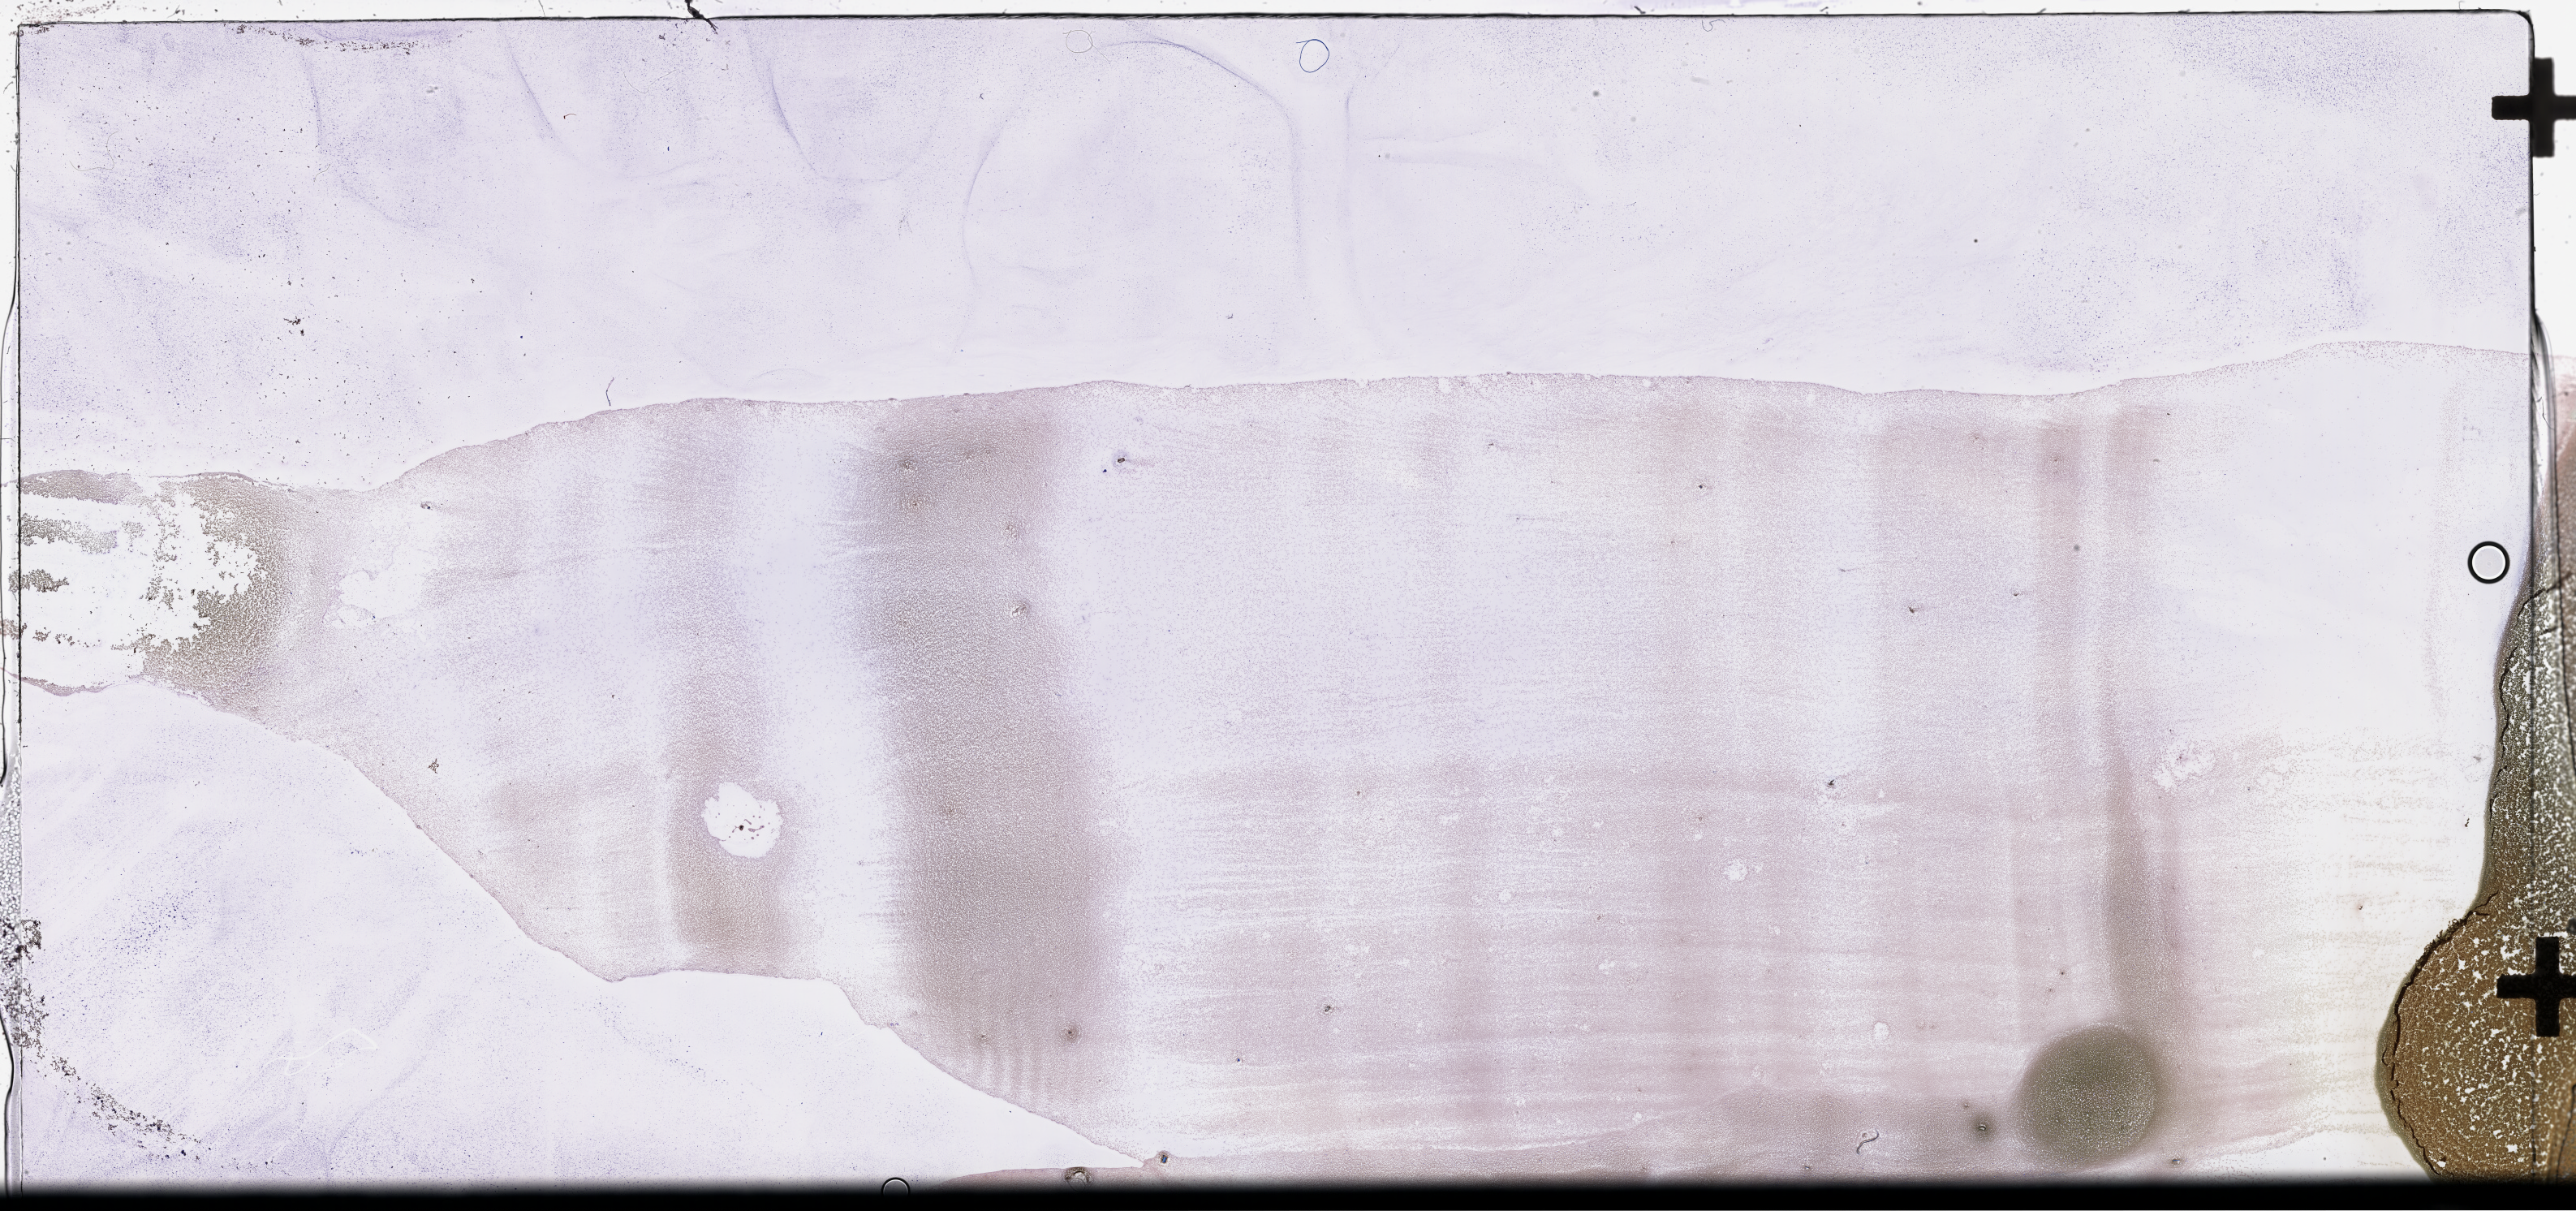
Wright-Giemsa-stained whole blood smear, whole-slide image, low-resolution overview of the scanned area, about 51.3 x 24.1 mm. Patient sex: male.
Patient diagnosis: Plasma Cell Myeloma.